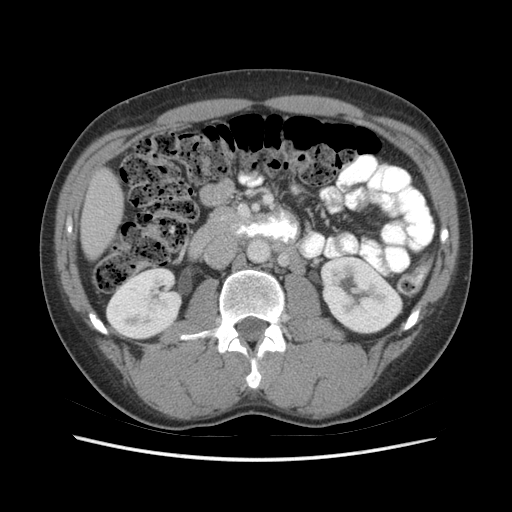
Contrast-enhanced abdominal CT (liver protocol), one axial slice. Slice 13 of 73 in the series (ordered by position). Soft-tissue window (W 400 / L 40 HU). 512 × 512 image matrix. Case-level facts recorded for this patient, not image findings: diagnosis: hepatocellular carcinoma (patient treated with transarterial chemoembolisation; whether this scan precedes or follows treatment is not stated here); TNM stage (as recorded): Stage-IIIA; Child-Pugh class: A; tumour size: 6.6 cm.
Structures marked on this image (semi-automatic segmentation, software-assisted and operator-edited):
- liver parenchyma outside the tumour (the mass and vessels are separate outlines, so this box may not span the whole liver): bounding box <80,168,122,258> (left, top, right, bottom; pixels)